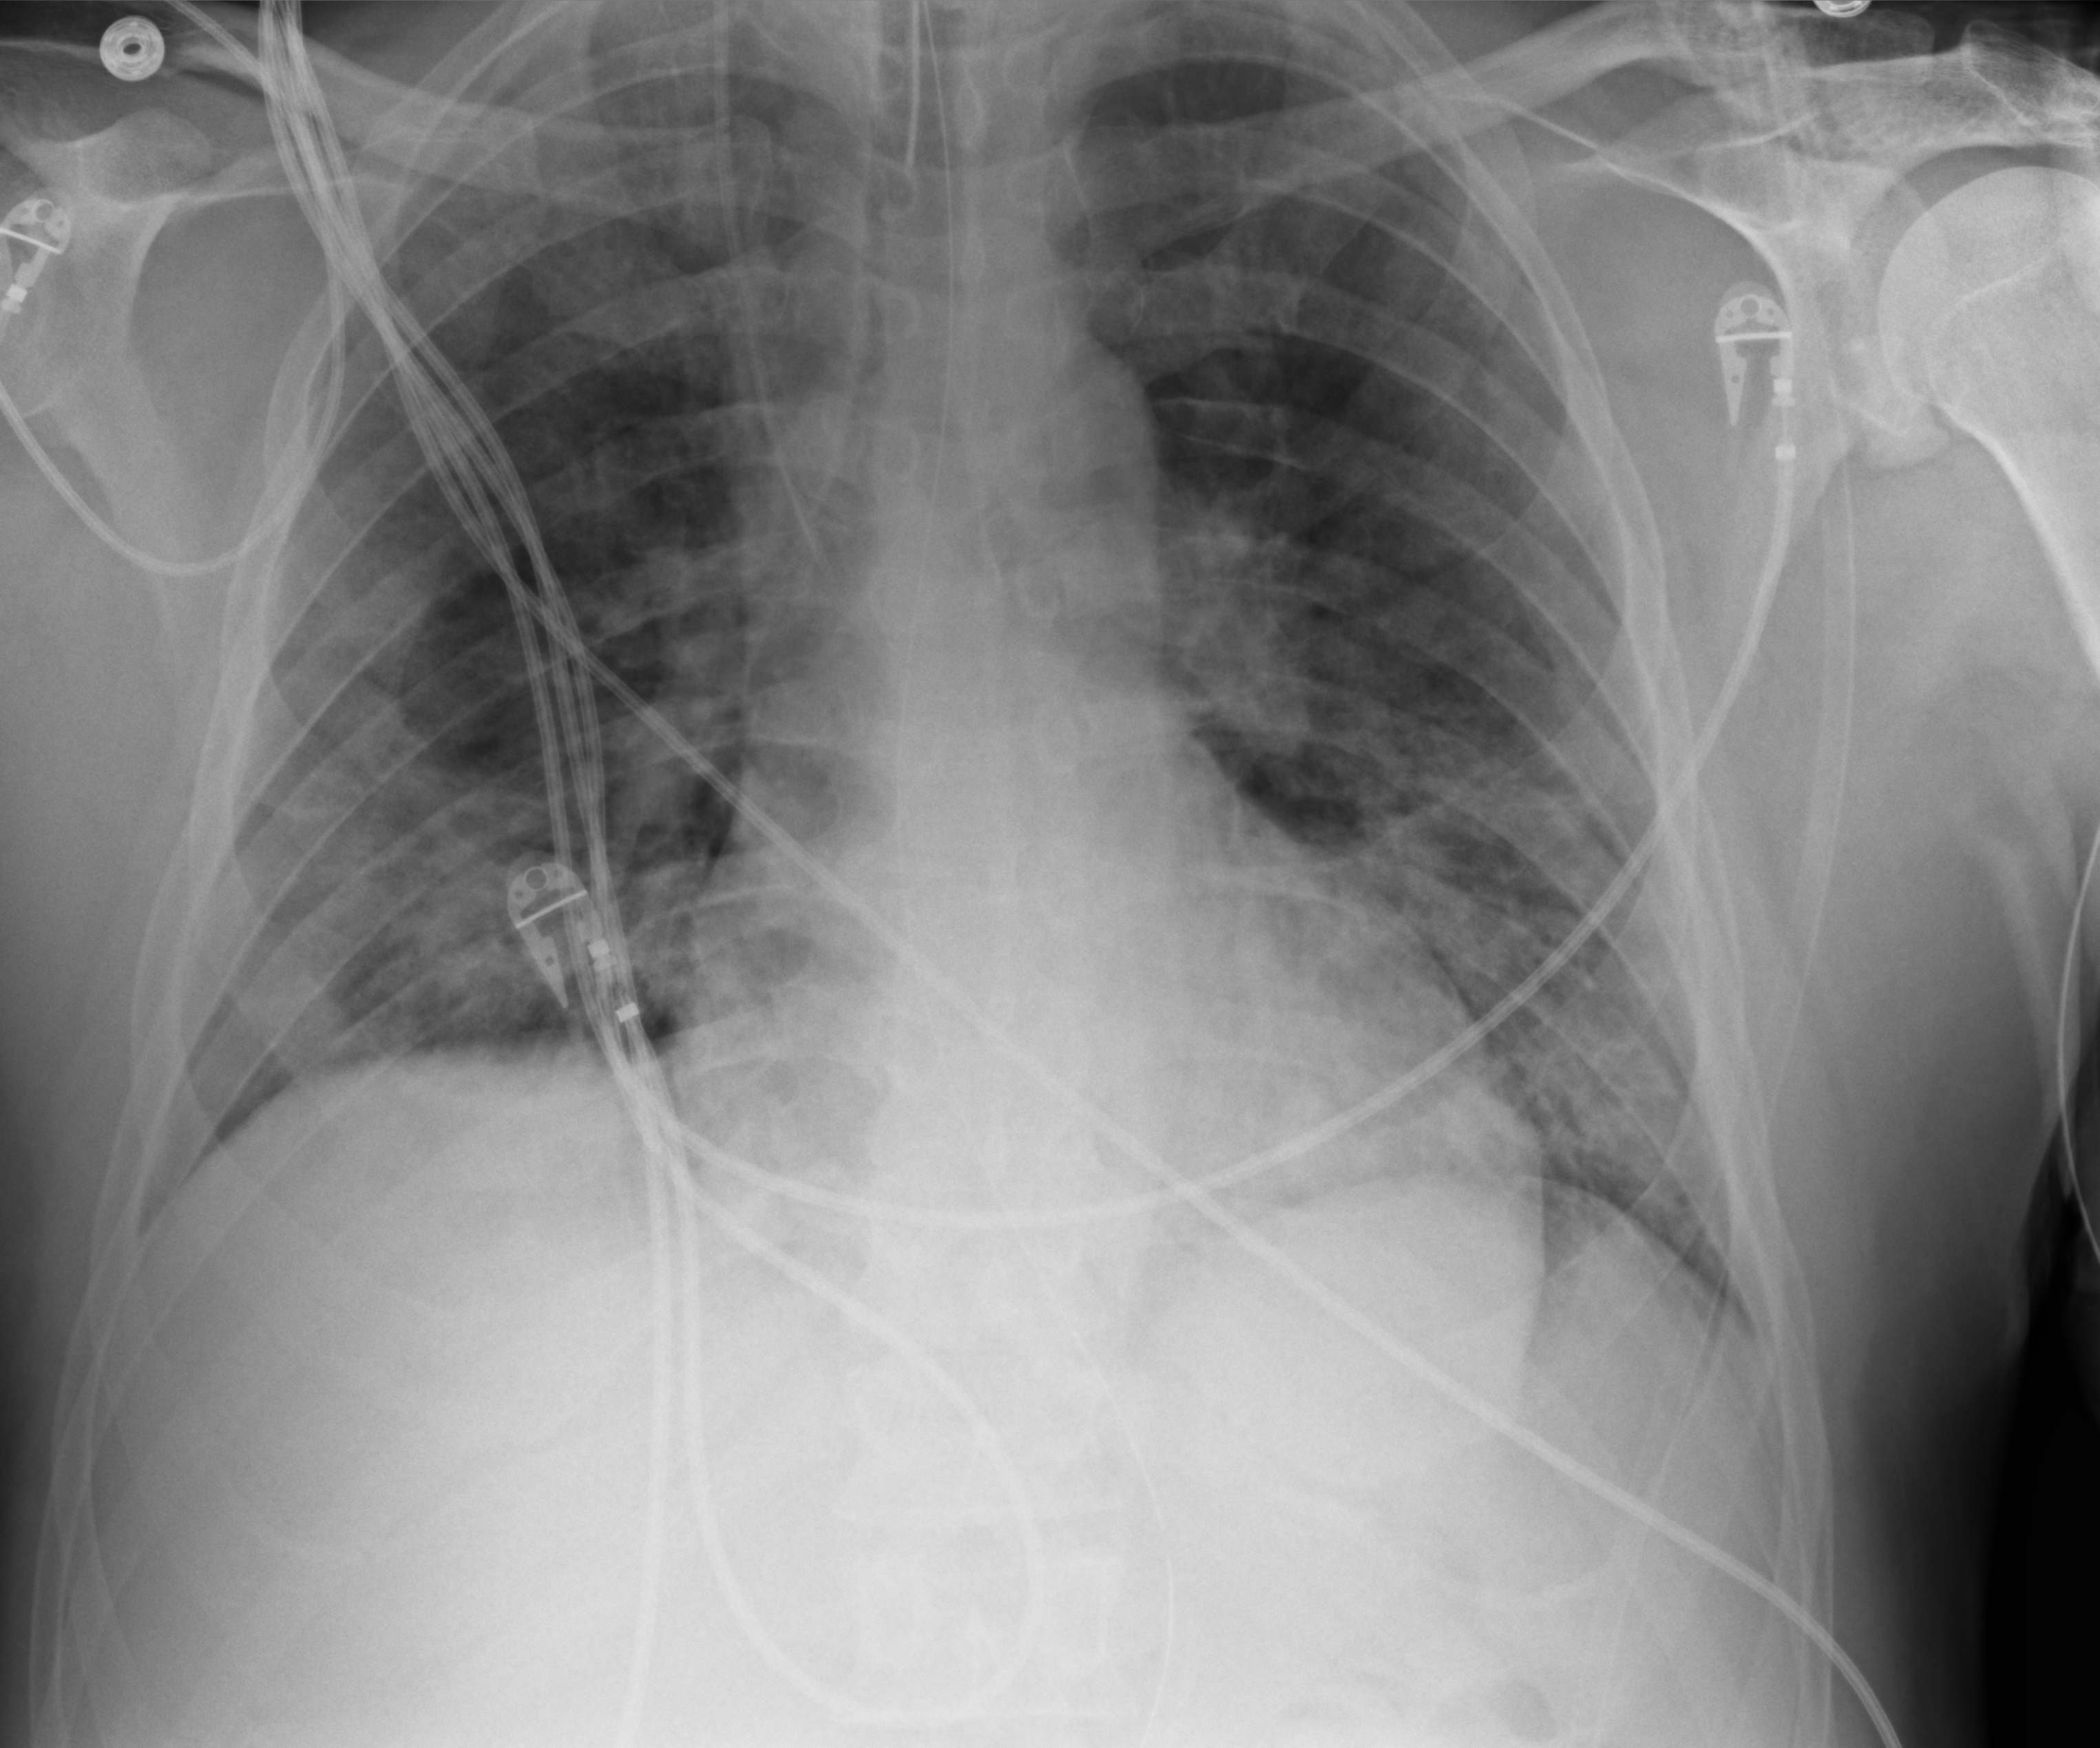
Portable chest radiograph; anteroposterior (AP) projection. Male patient hospitalised with COVID-19, age 18–59 years.
Admission-level facts for this patient (not findings on this image; timing relative to this image not recorded): admitted to intensive care during this hospital stay: no.